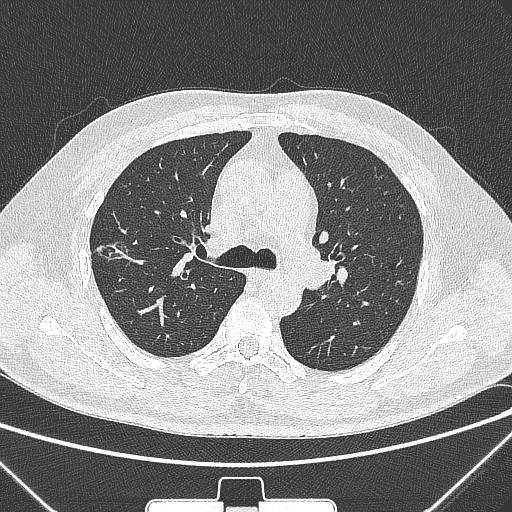
Chest CT, one axial slice. Slice 201 of 320 in the series (ordered by position). 120 kVp. Lung window (W 1500 / L -600 HU). 512 × 512 image matrix, field of view 350 × 350 mm. Patient: male, 58 years. Case-level facts recorded for this patient, not image findings: clinical TNM (as recorded): T1c N0 M0; histopathological grade: G2.
Annotated regions visible in this slice (bounding box drawn by a radiologist):
- lung tumour (recorded histology: adenocarcinoma): bounding box <88,231,133,271> (left, top, right, bottom; pixels)